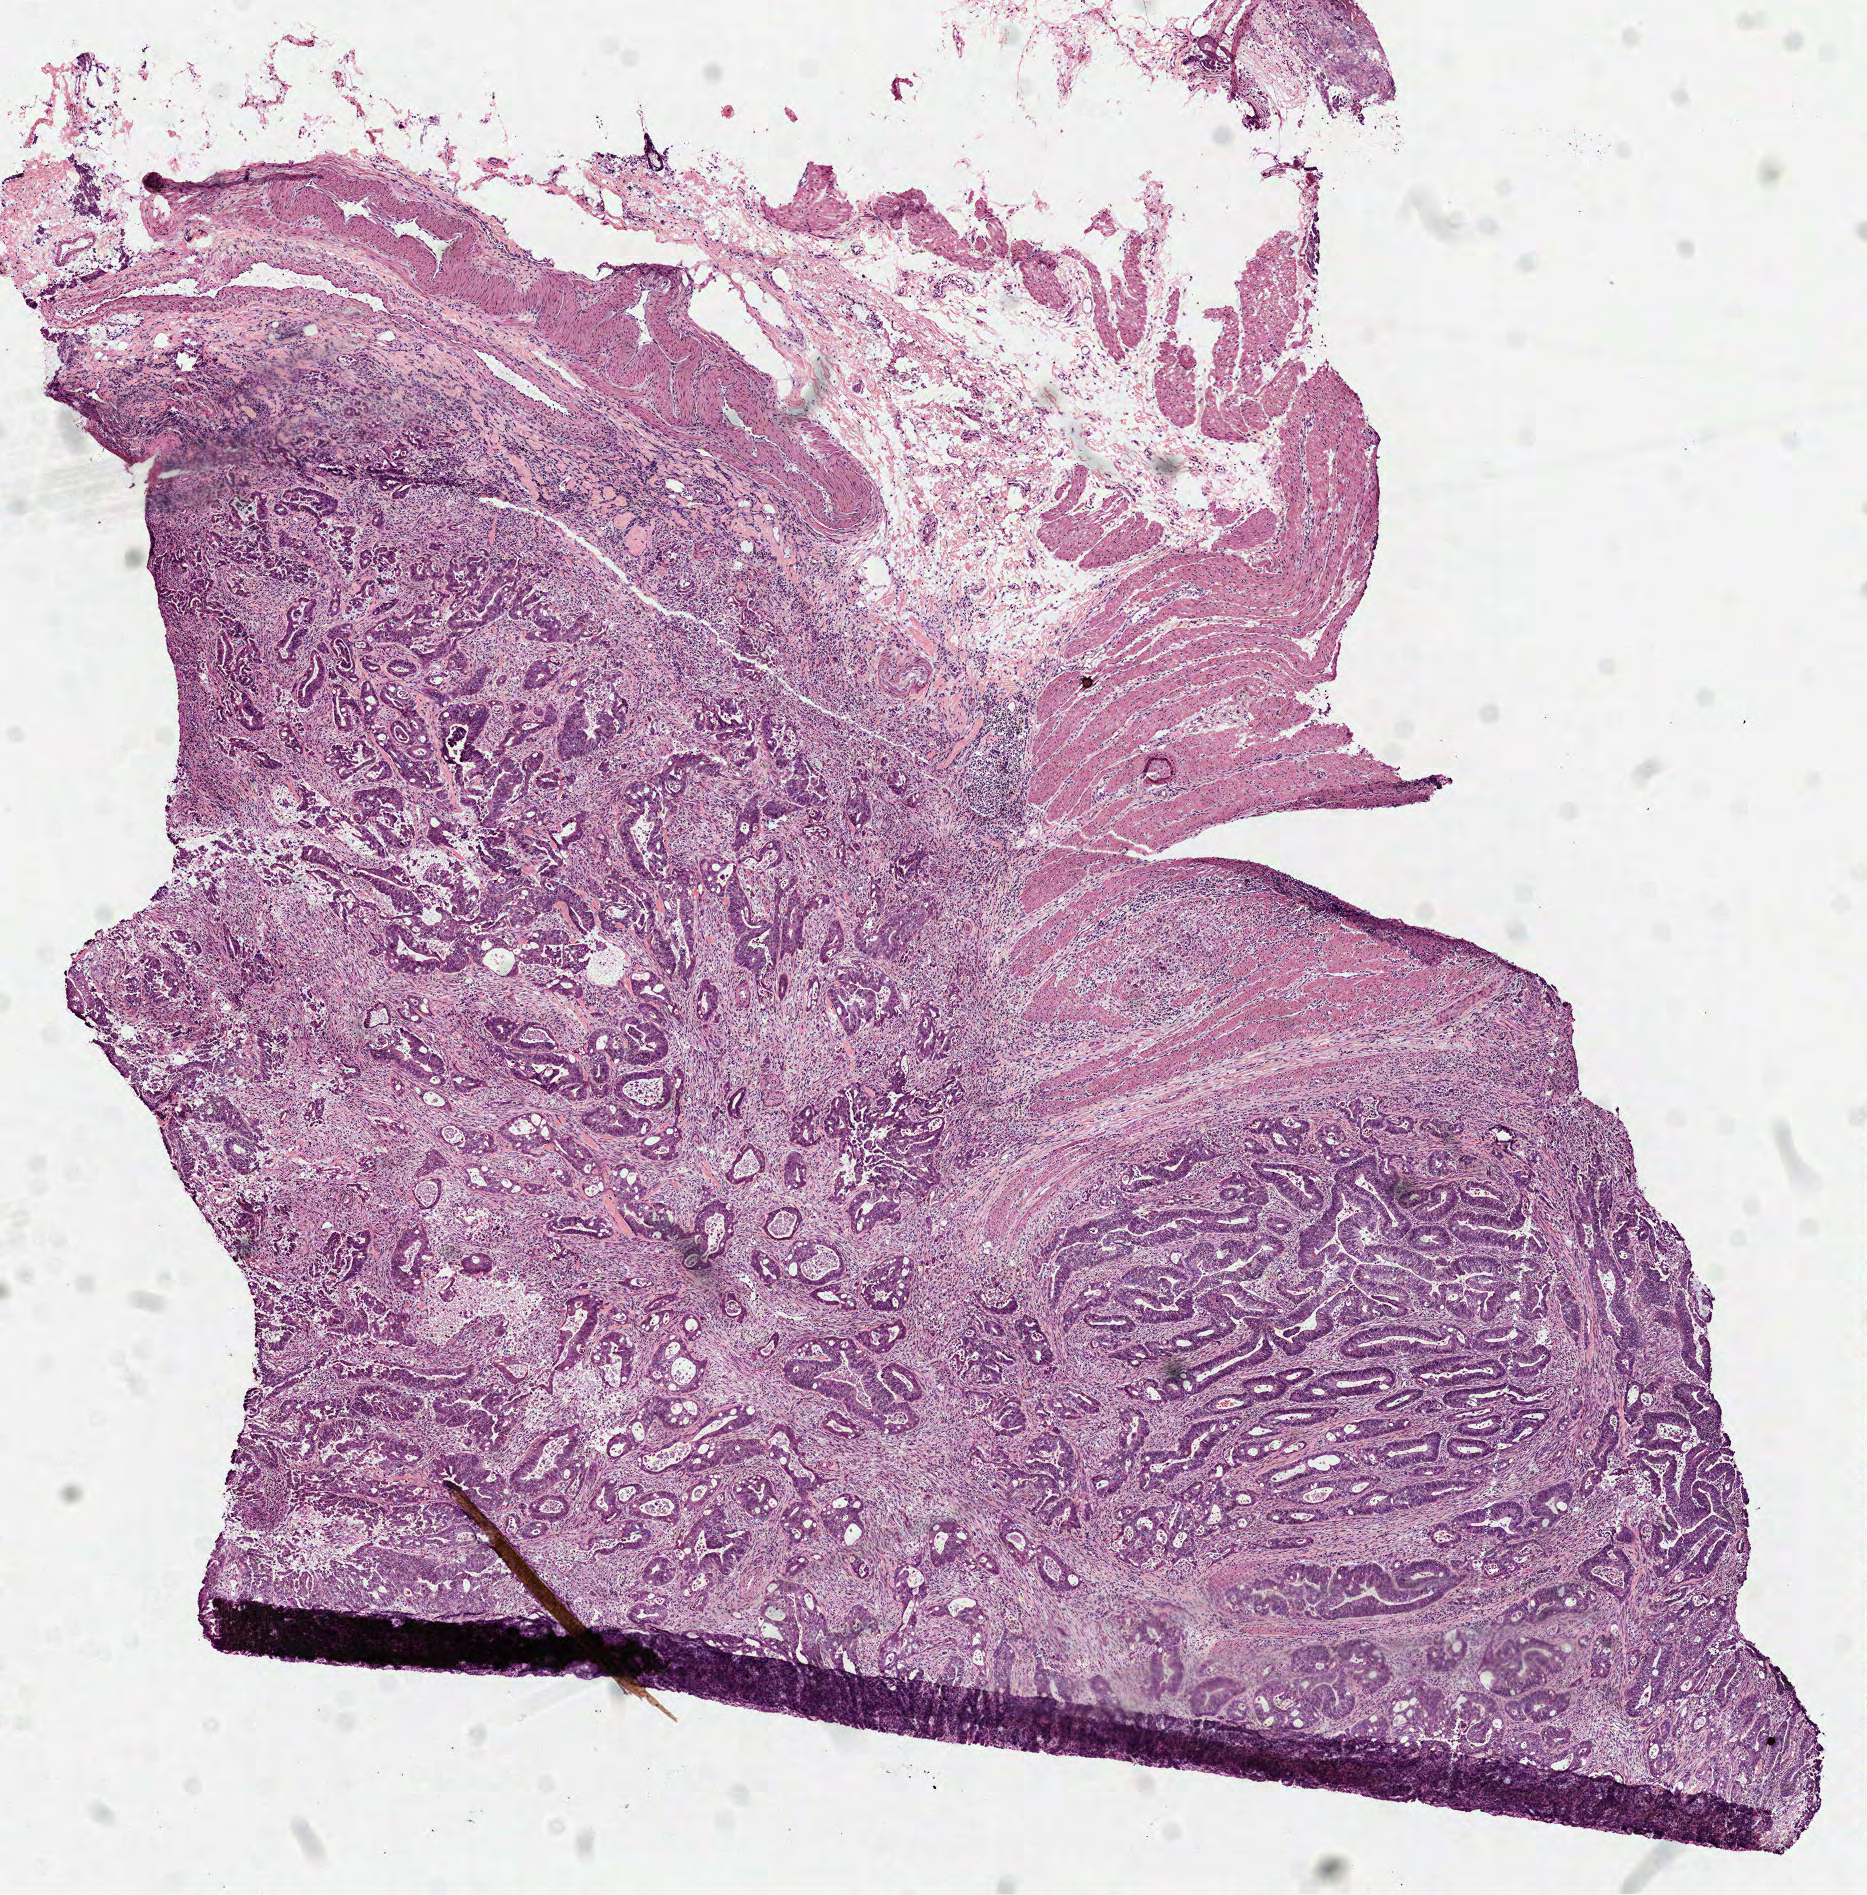
H&E whole-slide image, whole scanned area (about 7.5 x 7.6 mm, from a 40x scan) shown as a low-resolution overview, frozen section from the top of the tissue portion, colon, primary tumour sample. Patient sex: male. Composition of this section per pathologist review: tumour cells 69%, tumour nuclei 60%, normal cells 1%, stromal cells 30%, necrosis 0%.
Pathologic diagnosis: Adenocarcinoma, NOS (ascending colon). AJCC pathologic stage: IIA.